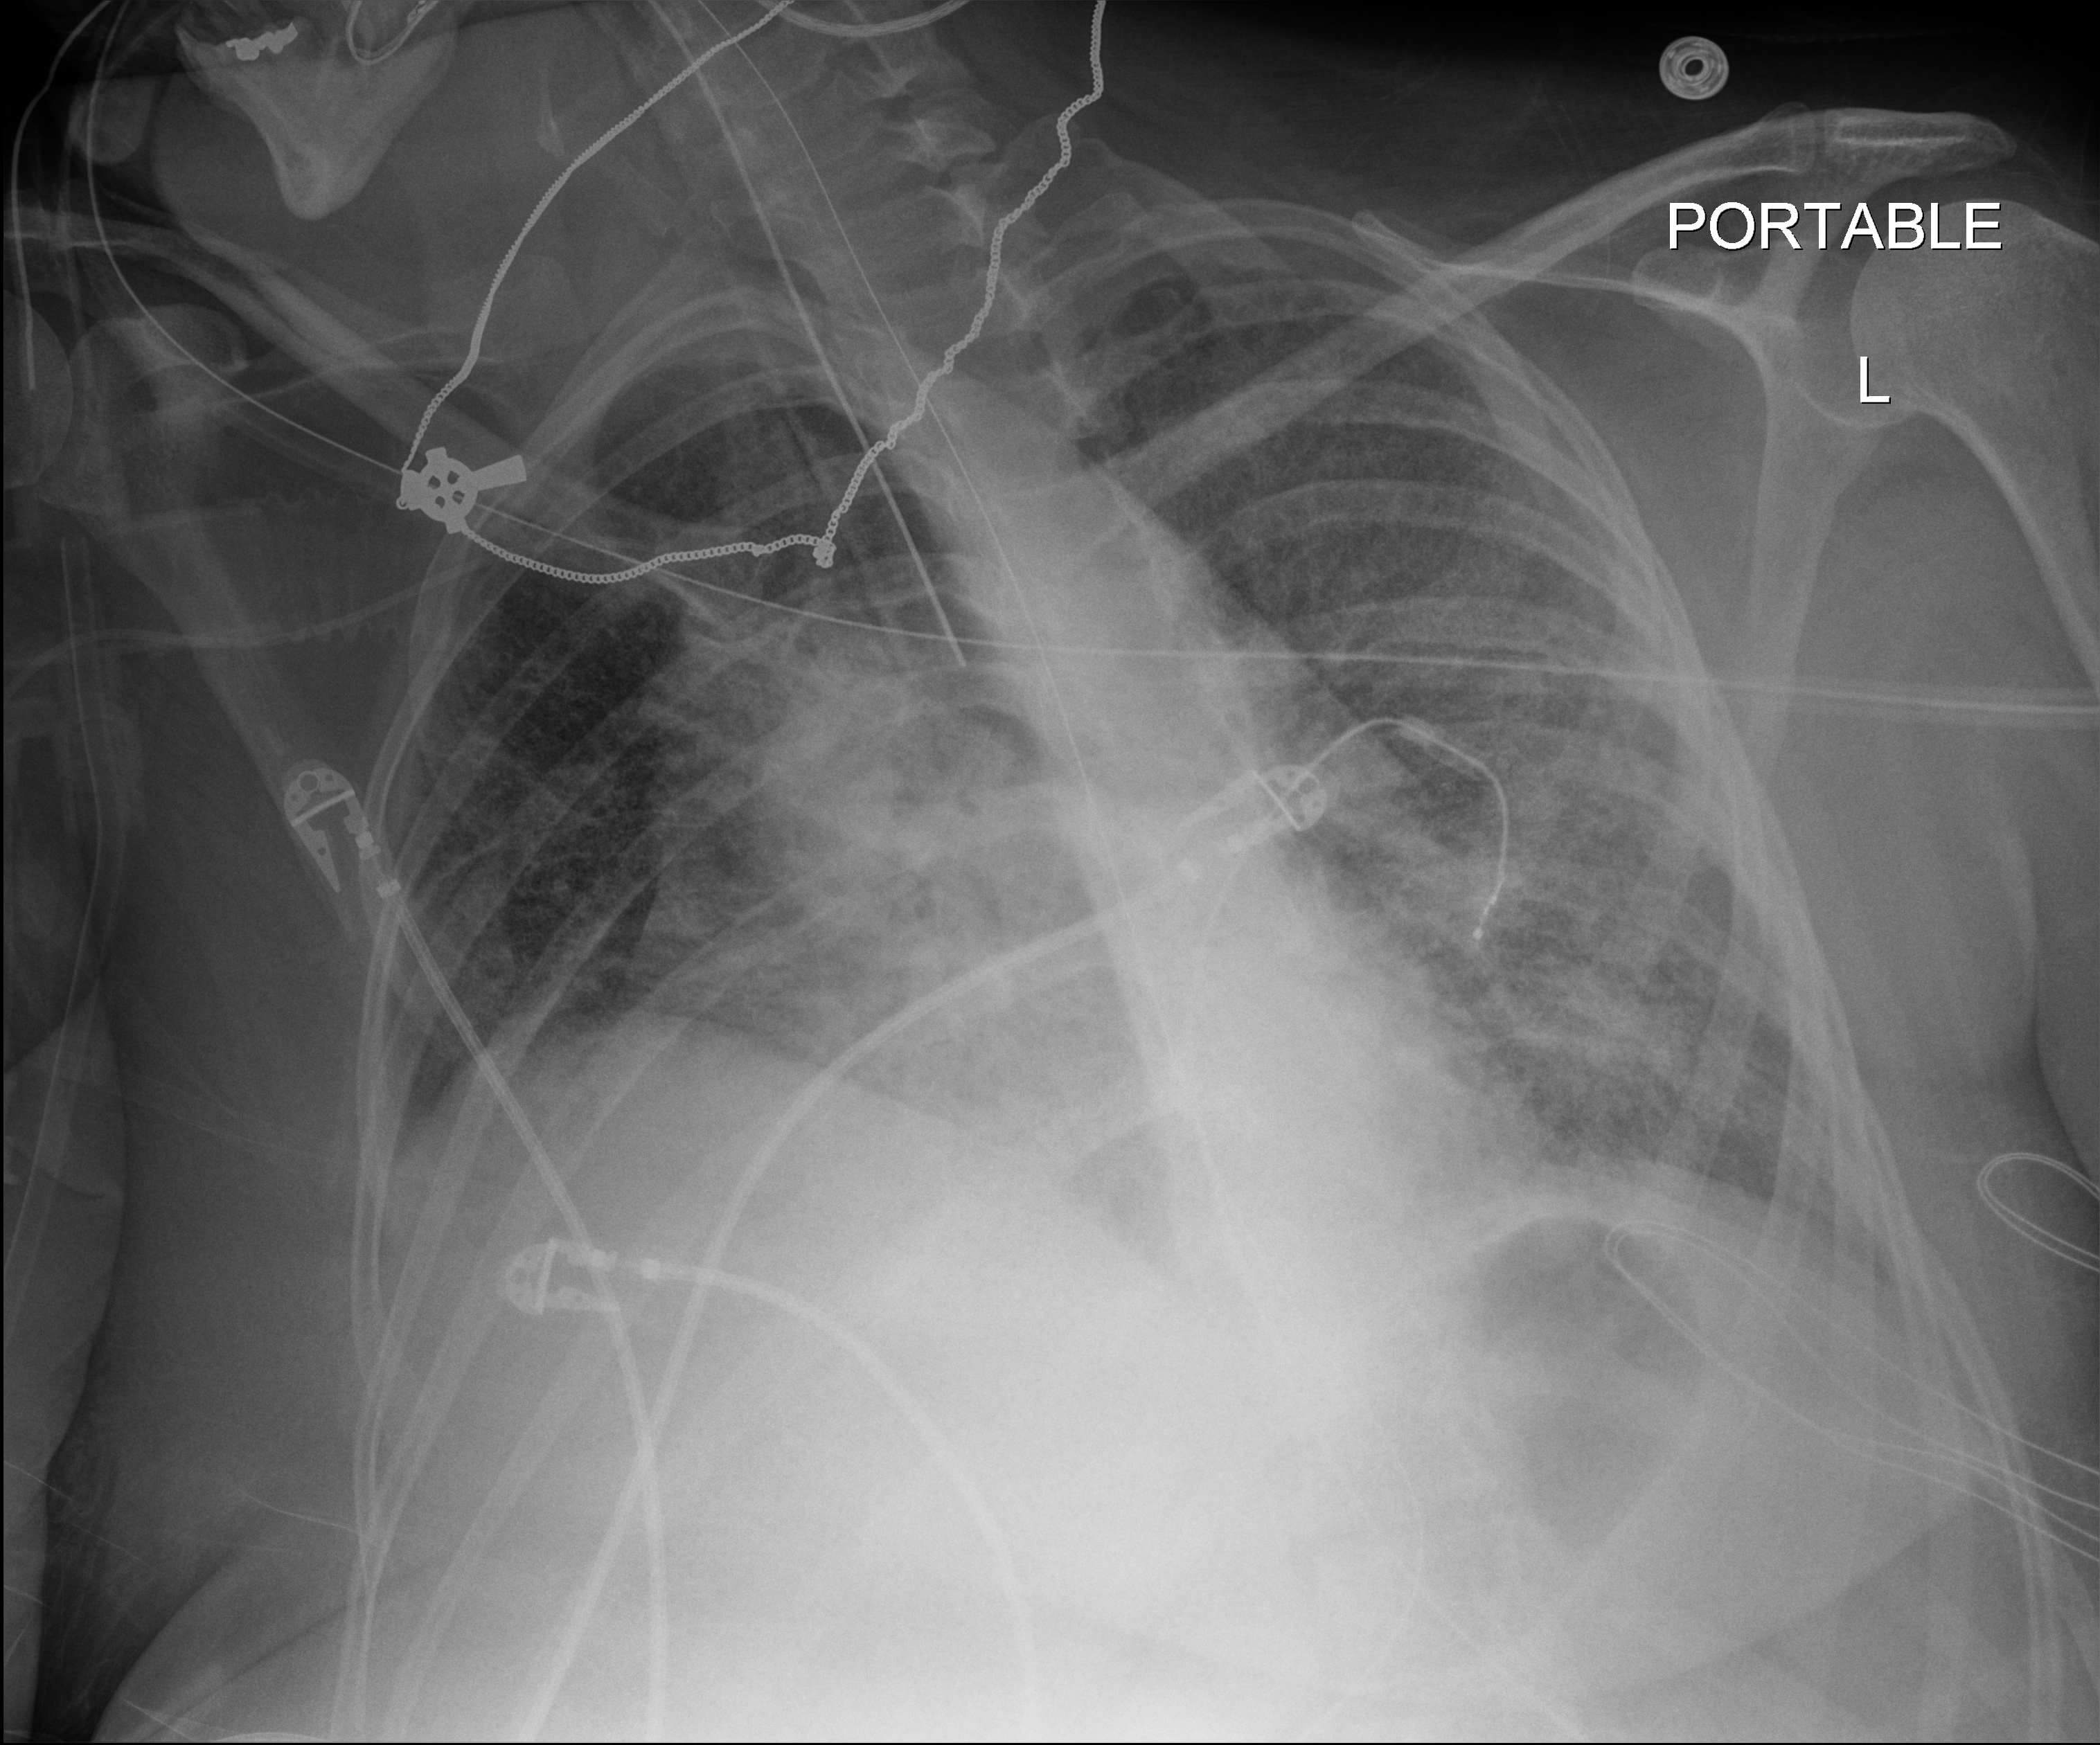
Chest radiograph (digital radiography); anteroposterior (AP) projection. Patient hospitalised with COVID-19; female, aged 18–59 years.
From the hospital-stay record, not from the radiograph (when in the stay this image was taken is not recorded): admitted to intensive care during this hospital stay: yes; length of hospital stay: 73 days.